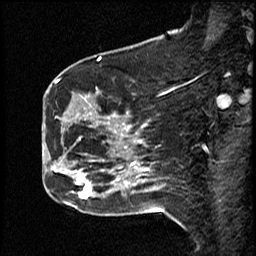
Breast MRI (dynamic contrast-enhanced), one sagittal slice; slice 18 of 50 in the series (ordered by position); dynamic contrast-enhanced study with each time point stored as its own series, time point 2 of 4 at this slice position (early post-contrast, ordered by acquisition time); 1.5 T; TE 4.2 ms, TR 18.5 ms; 3 mm slice thickness; 256 × 256 image matrix, field of view 200 × 200 mm. Female patient, age 44 years. Case-level facts recorded for this patient, not image findings: setting: breast cancer imaged before/during neoadjuvant chemotherapy; receptor status: HR-positive, HER2-negative.
Outlined on this slice (semi-automatically segmented with operator editing):
- analysis volume of interest (the breast-tissue region the enhancement analysis was run in; not a lesion): bounding box [x1, y1, x2, y2] px = [59, 80, 114, 206]
- tumour enhancement mask (voxels above the 100 % enhancement threshold inside the analysis volume of interest): [72, 173, 92, 198]